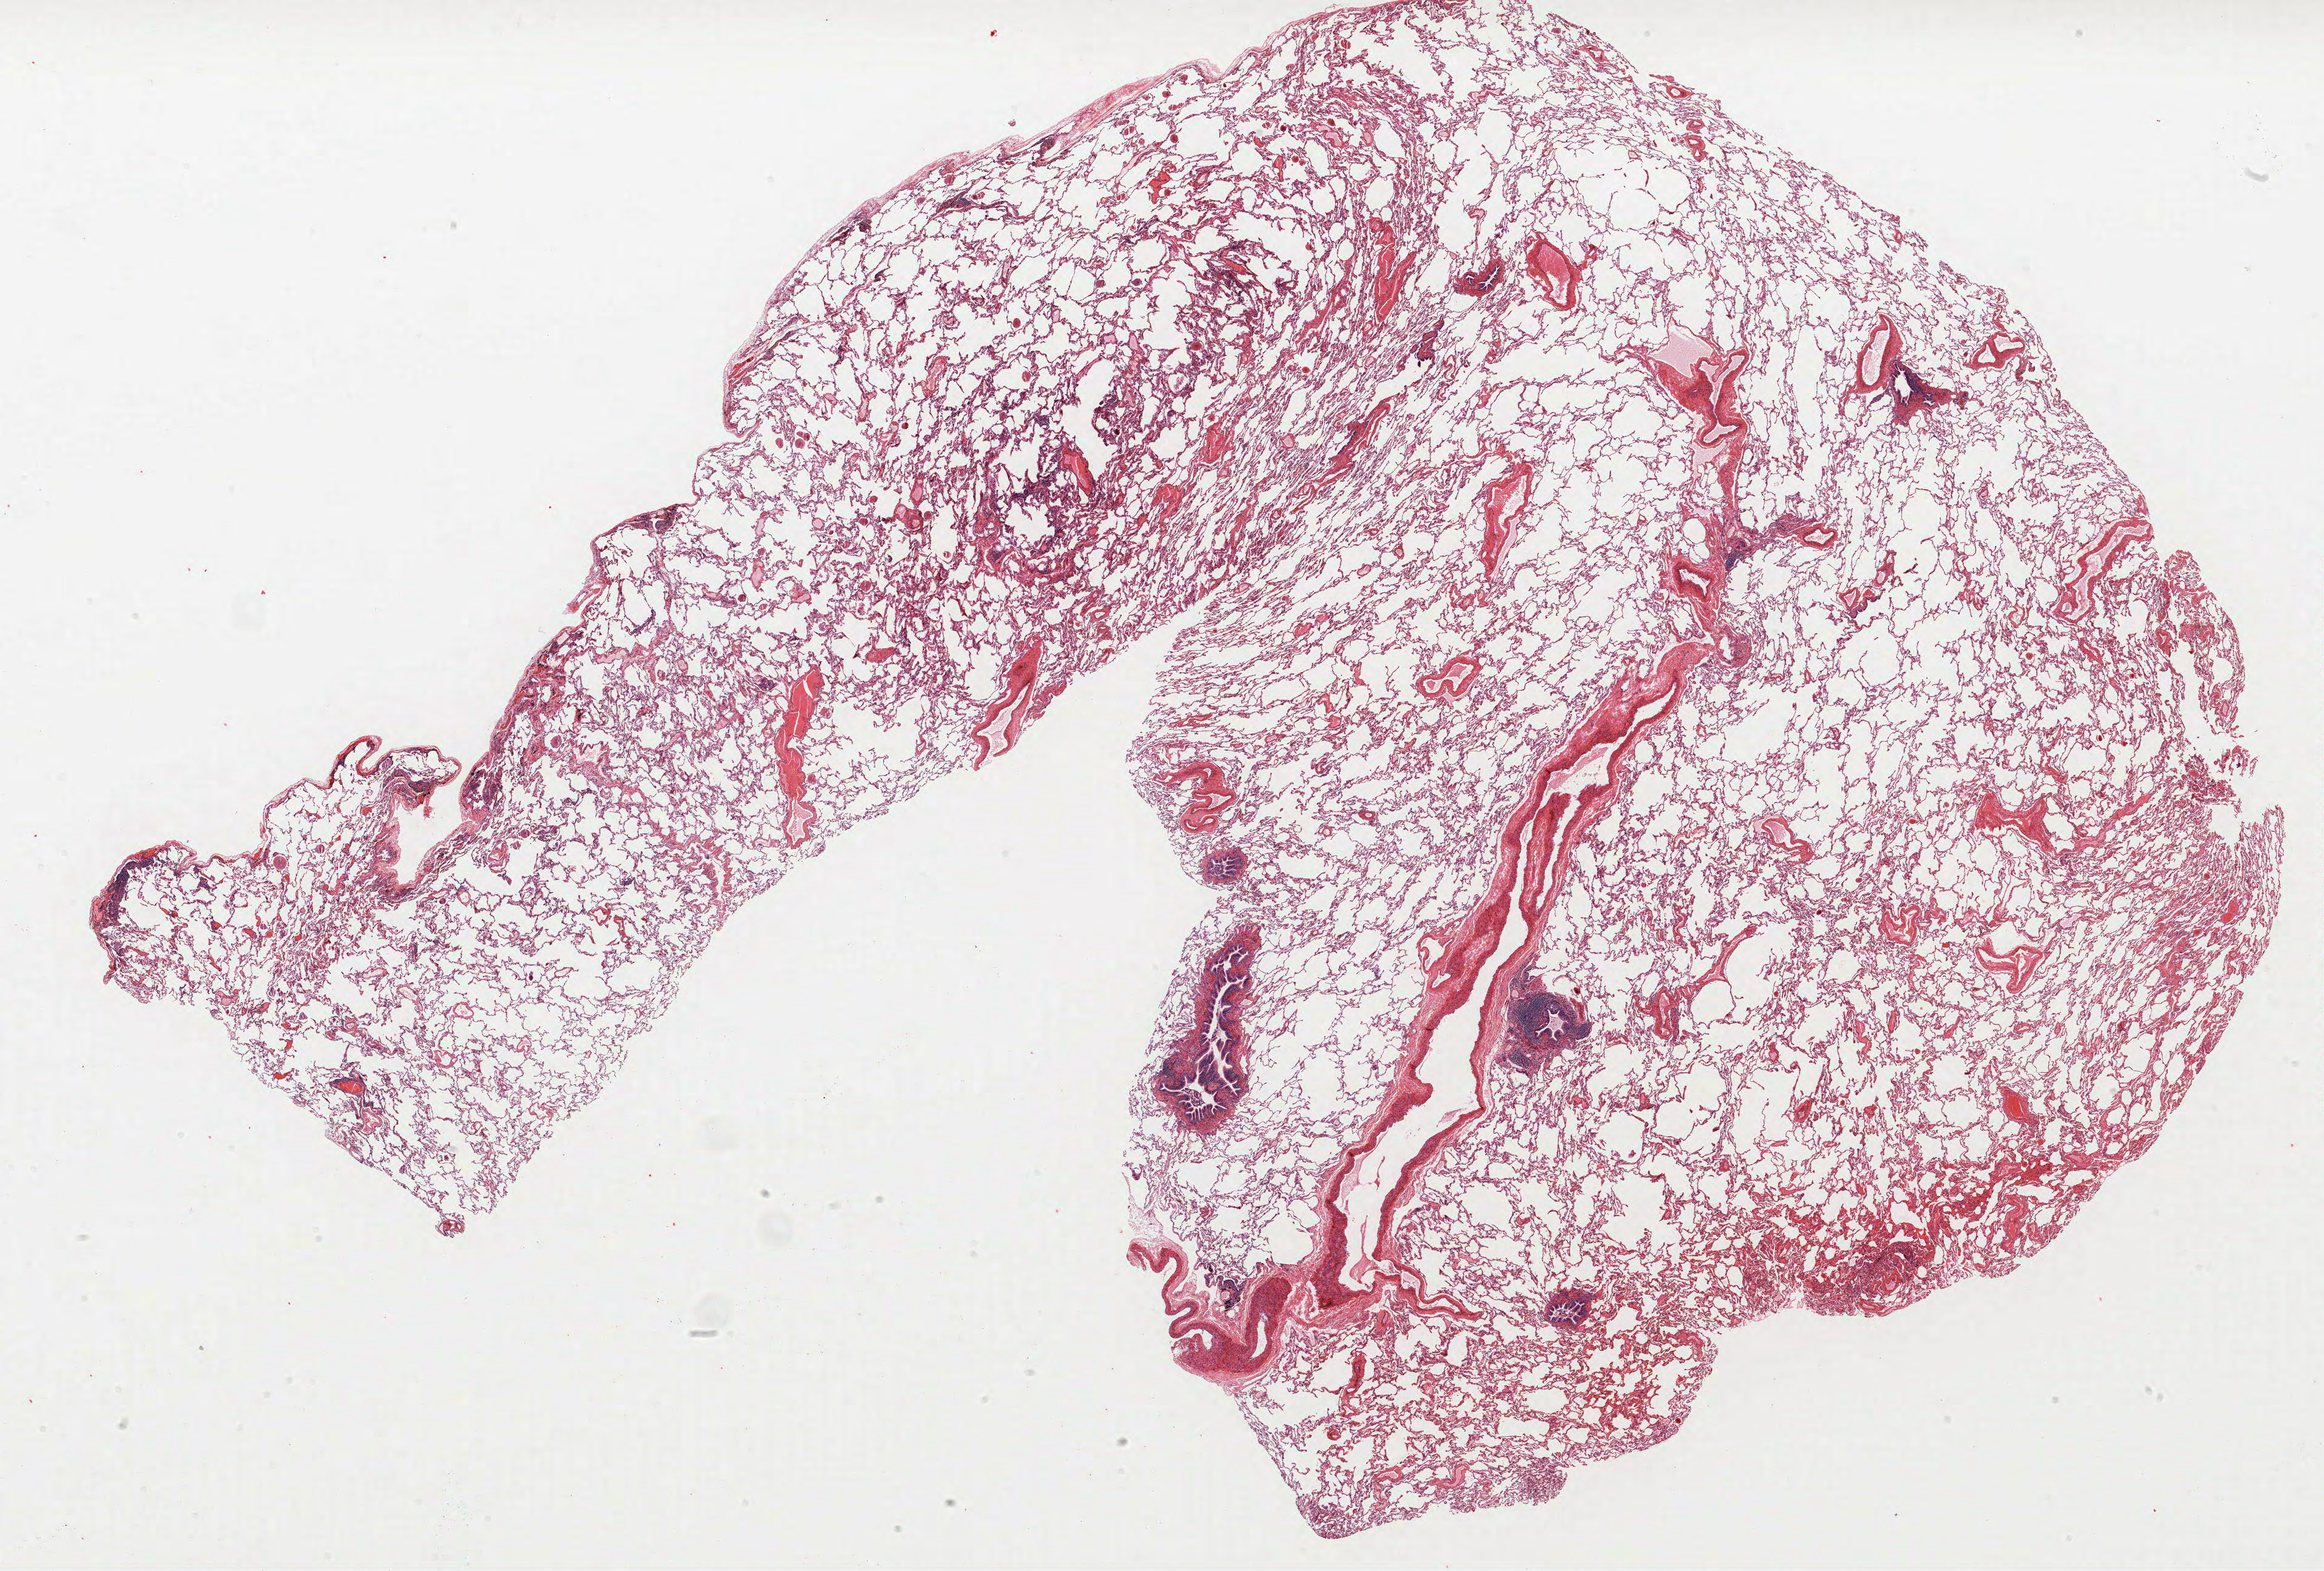
Whole-slide histology image, H&E-stained — shown as a low-resolution overview of the whole scanned area (about 30.5 x 20.6 mm, slide scanned at 40x), formalin-fixed paraffin-embedded (FFPE) section, lung. Female, age 55 at enrolment.
Tumour size (pathology): 10 mm. Primary tumour location (clinical record): left lower lobe. Stage (AJCC 7th edition): IA. Participant's lung-cancer diagnosis: Carcinoid tumor, NOS (ICD-O-3 8240/3).